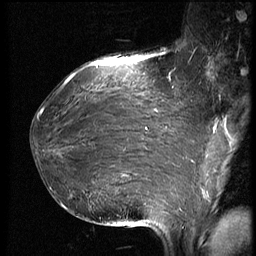
Breast MRI (dynamic contrast-enhanced), one sagittal slice. Slice 29 of 66 in the series (ordered by position). Dynamic contrast-enhanced series, image 2 of 3 at this slice position (ordered by acquisition). 1.5 T. TE 4.2 ms, TR 8.9 ms. 2.5 mm slice thickness. 256 × 256 image matrix. Female patient, age 39 years. From the clinical record (not read from this slice): setting: breast cancer imaged before/during neoadjuvant chemotherapy; receptor status: HER2-positive.
Structures marked on this image (semi-automatic segmentation, software-assisted and operator-edited):
- analysis volume of interest (the breast-tissue region the enhancement analysis was run in; not a lesion): bounding box [x1, y1, x2, y2] px = [32, 75, 188, 218]
- tumour enhancement mask (voxels above the 140 % enhancement threshold inside the analysis volume of interest): [65, 75, 147, 211]